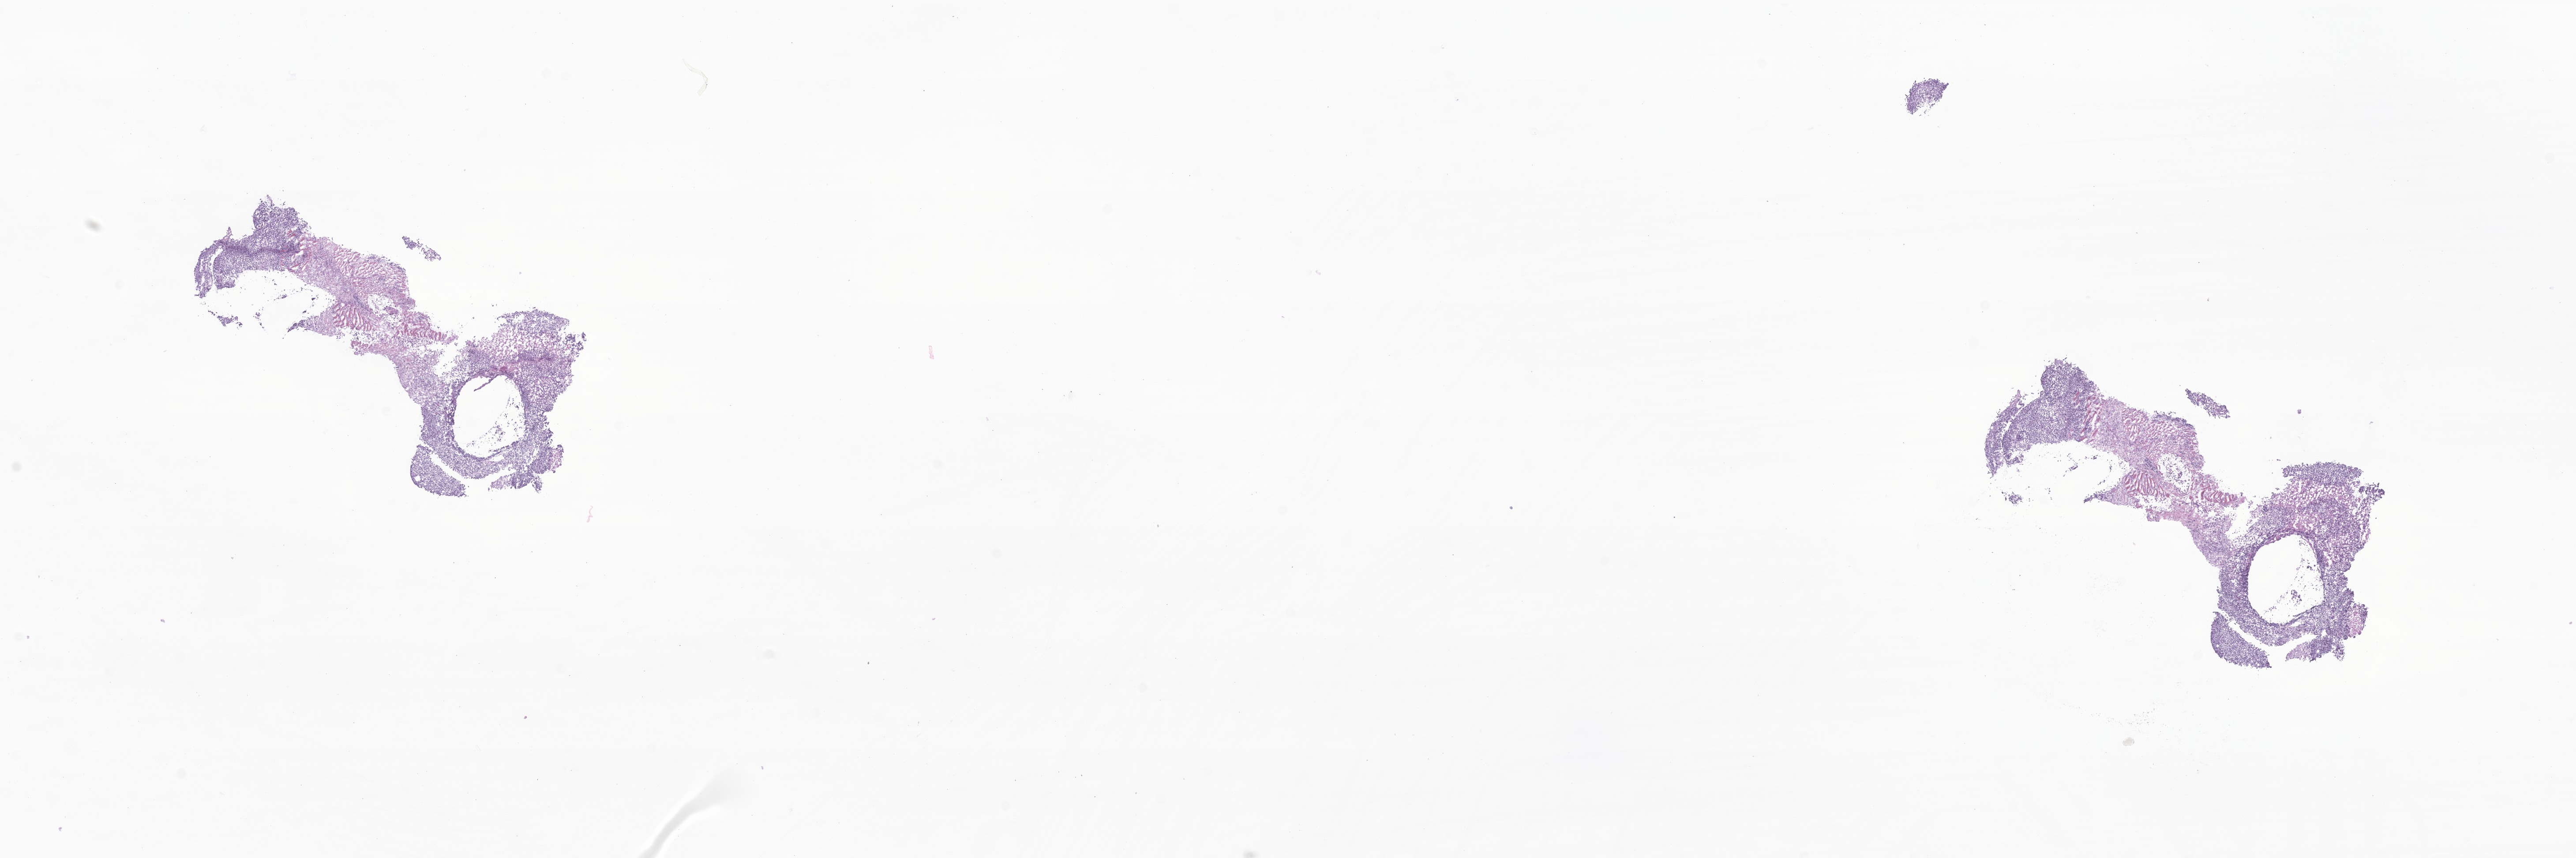
Whole-slide image, haematoxylin and eosin stain of tumor tissue from the retroperitoneum — low-resolution overview of the scanned area, about 24.6 x 8.2 mm, cryosection (OCT / tissue freezing medium). Patient female; age 125 months.
* recorded diagnosis: Alveolar rhabdomyosarcoma